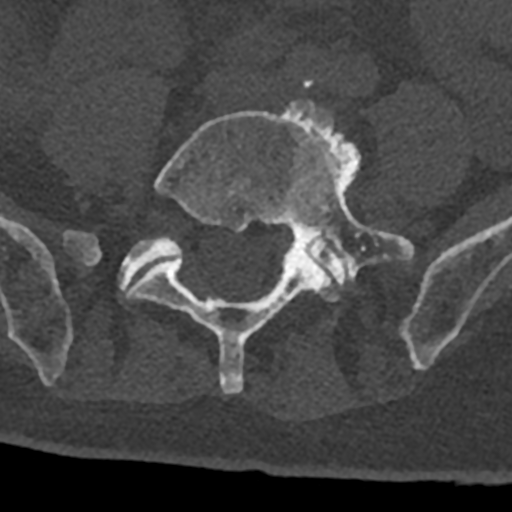
CT including the spine, one axial slice. Position 197 of 797 along the scan axis. Bone window (W 1800 / L 400 HU). 0.5 mm slice thickness. 512 × 512 image matrix, field of view 160 × 160 mm. Male patient, age 74 years. Case-level facts recorded for this patient, not image findings: primary cancer: renal.
Outlined on this slice (semi-automatically segmented with operator editing):
- L5 vertebra: bounding box [x1, y1, x2, y2] px = [127, 100, 414, 394]